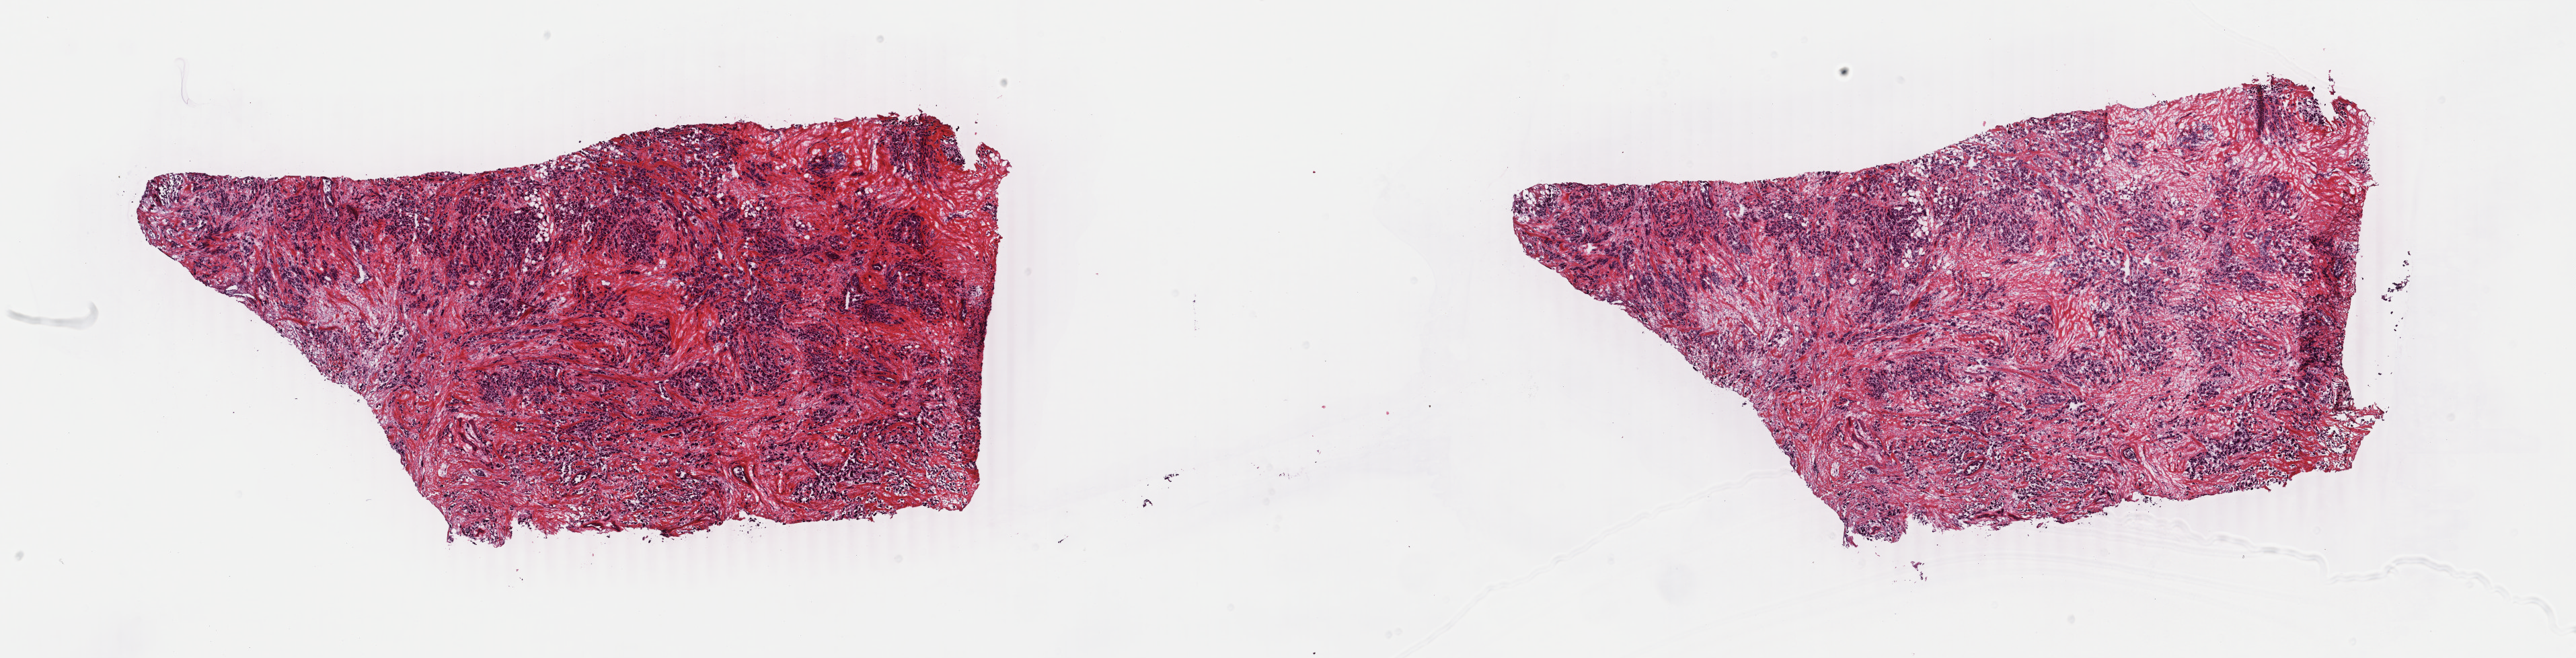
Digitized Hematoxylin and eosin (H&E) stained tissue section (whole slide), shown as a low-resolution overview of the whole scanned area (about 30.5 x 7.8 mm, acquisition: 40x scan). Frozen section from the top of the tissue portion. Primary tumour sample from the breast. Patient: female, age at initial diagnosis 46 years. Composition of this section per pathologist review: tumour cells 90%, tumour nuclei 90%, normal cells 1%, stromal cells 9%, necrosis 0%. Infiltration values recorded for this section: lymphocyte infiltration 1%, monocyte infiltration 0%, neutrophil infiltration 0%.
Histologic diagnosis: Infiltrating duct carcinoma, NOS. Laterality: right.